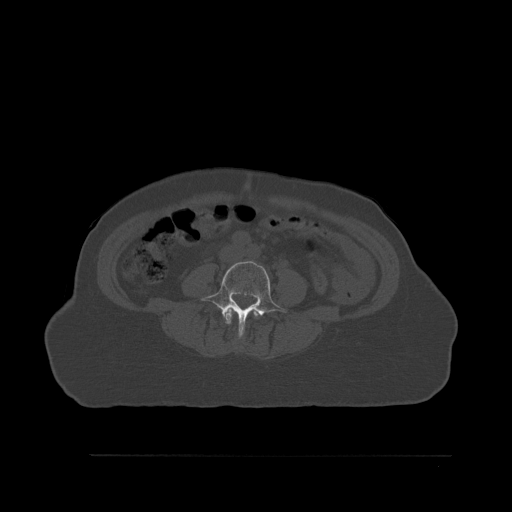
CT including the spine, one axial slice; position 209 of 527 along the scan axis; bone window (W 1800 / L 400 HU); 1.5 mm slice thickness; 512 × 512 image matrix, field of view 470 × 470 mm. Female patient, age 73 years. From the clinical record (not read from this slice): primary cancer: breast; vertebrae with lytic lesions (as recorded): L2.
Annotated regions visible in this slice (semi-automatic segmentation, software-assisted and operator-edited):
- L3 vertebra: box from (x=225, y=307) to (x=259, y=325) px
- L4 vertebra: (x=200, y=261)–(x=287, y=339)